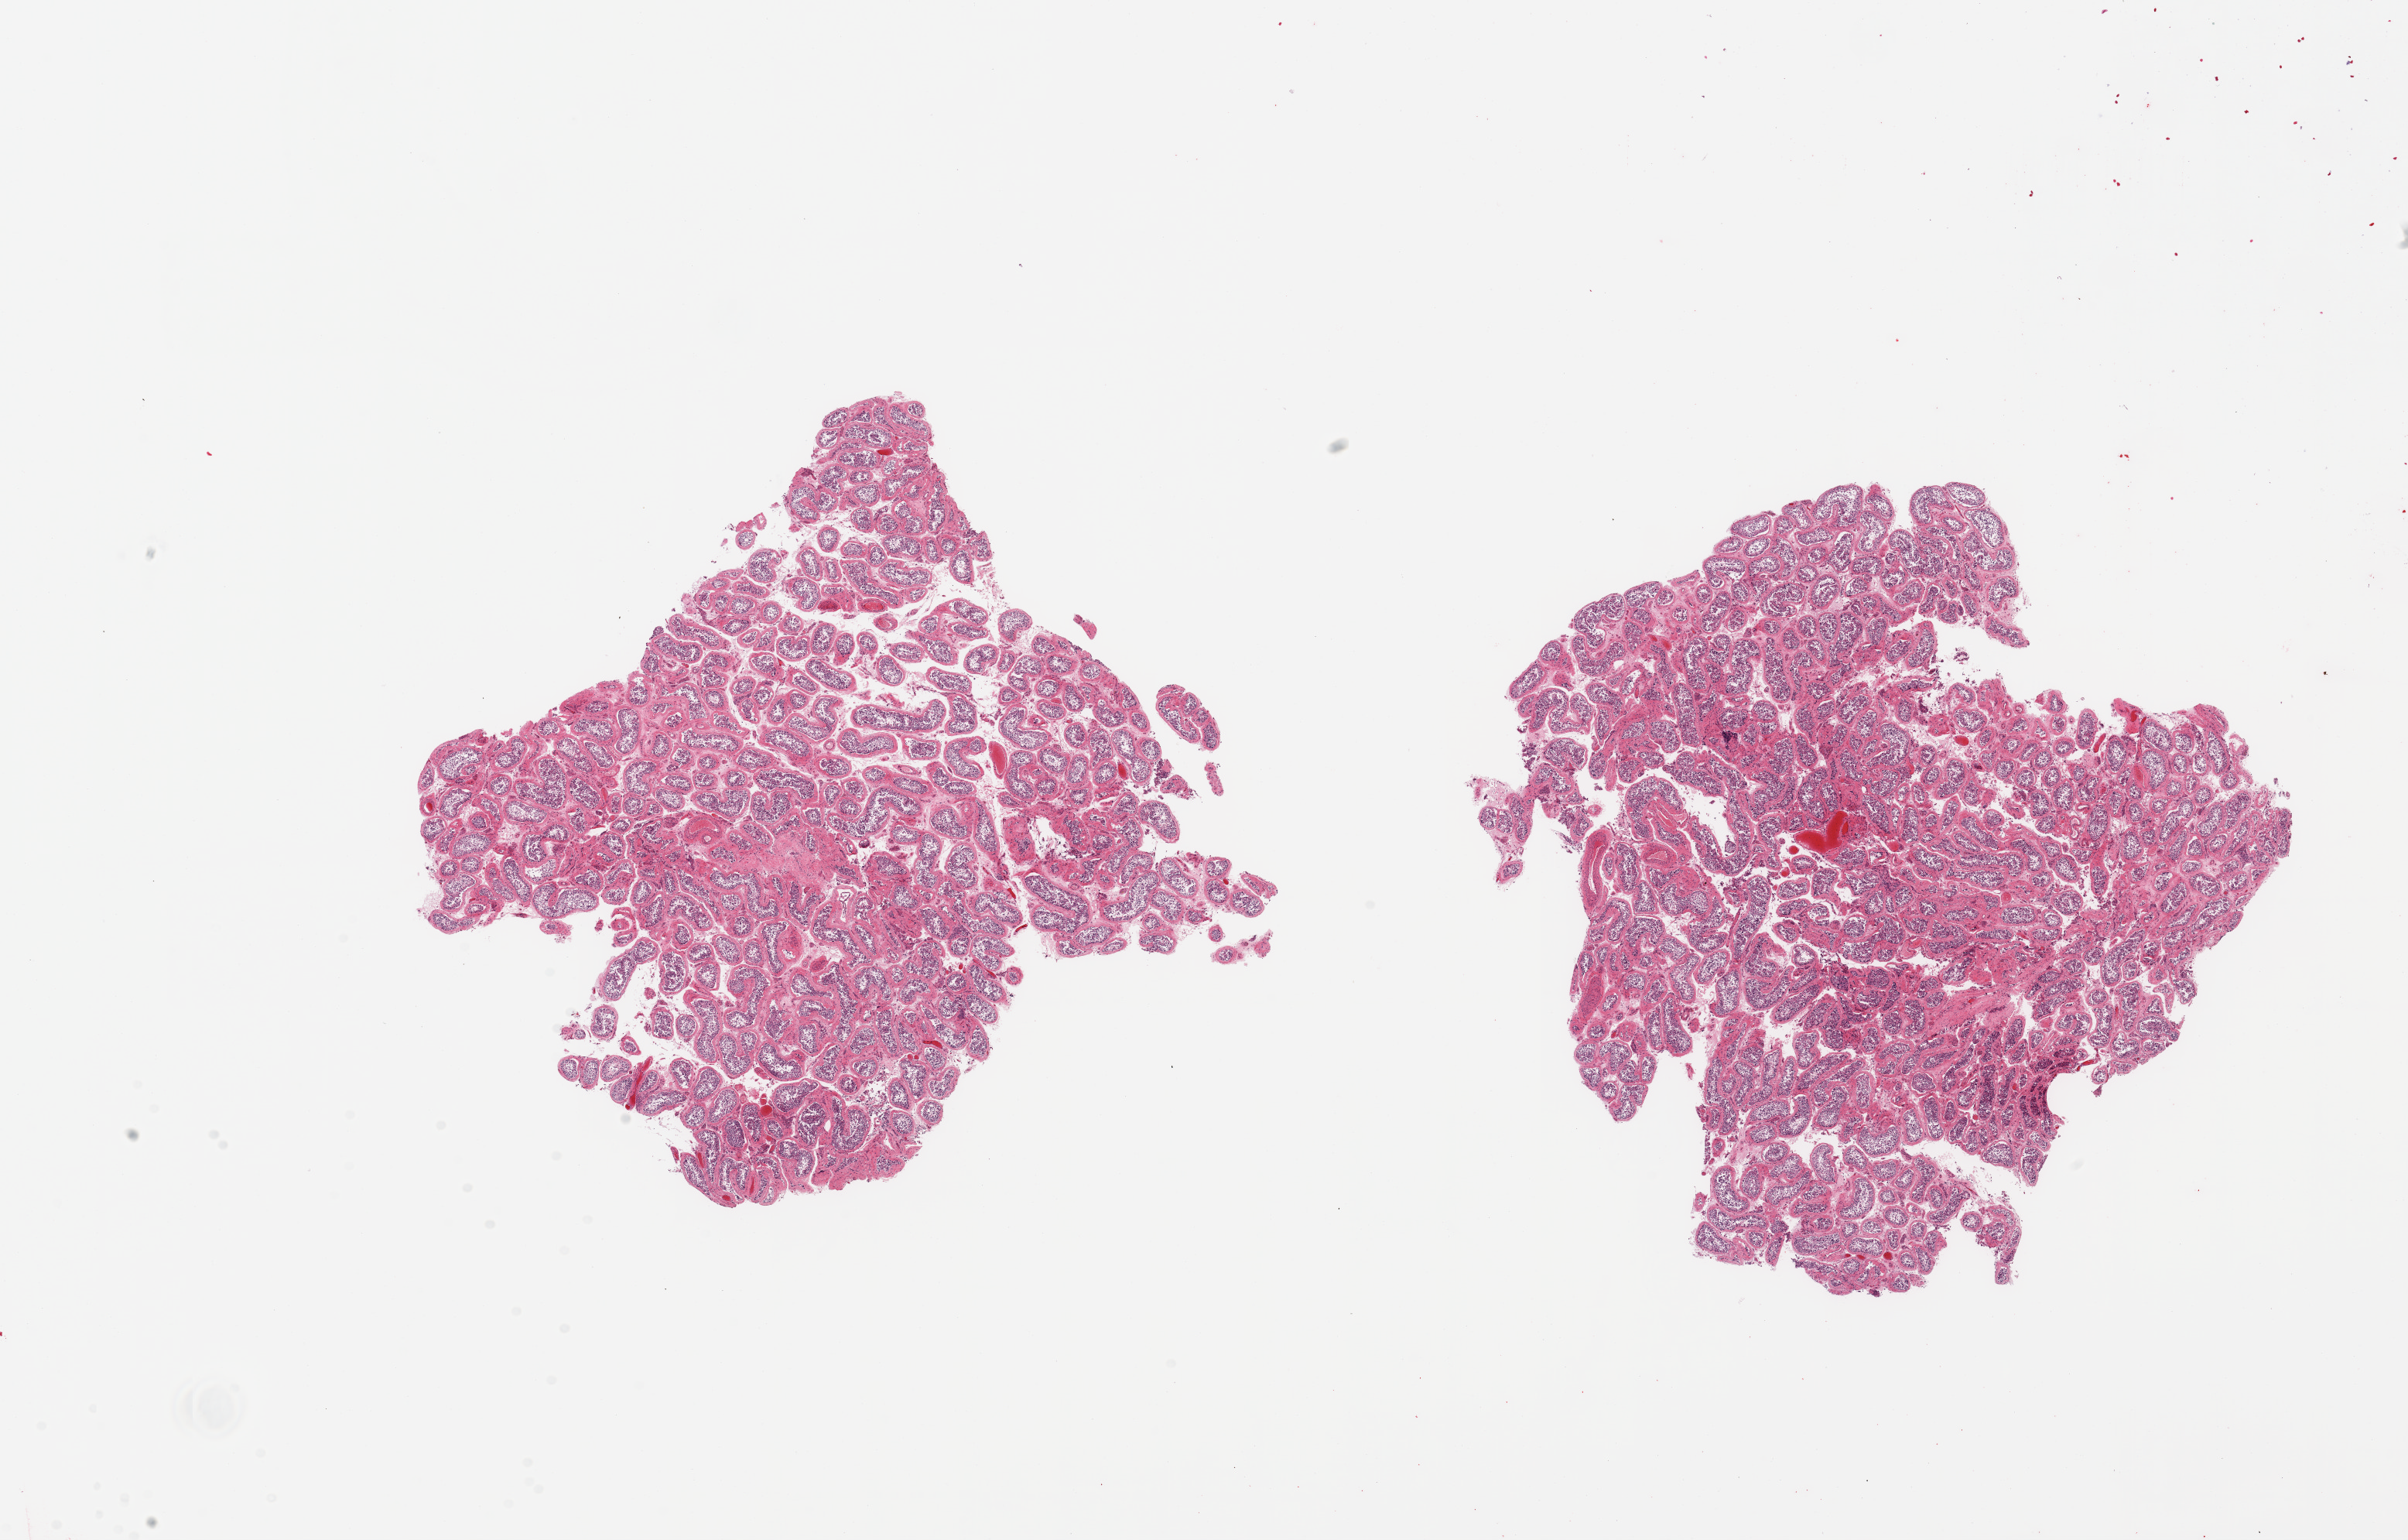
Digitized hematoxylin and eosin (H&E)-stained section, a low-resolution overview of the entire scanned area, about 24.6 x 15.7 mm (slide scanned at 20x). PAXgene-fixed, paraffin-embedded tissue. Target tissue: testis. Donor tissue sample. Donor sex: male.
Reviewer comment on this tissue sample: 2 pieces; active spermatogenesis; rare sclerotic tubules.